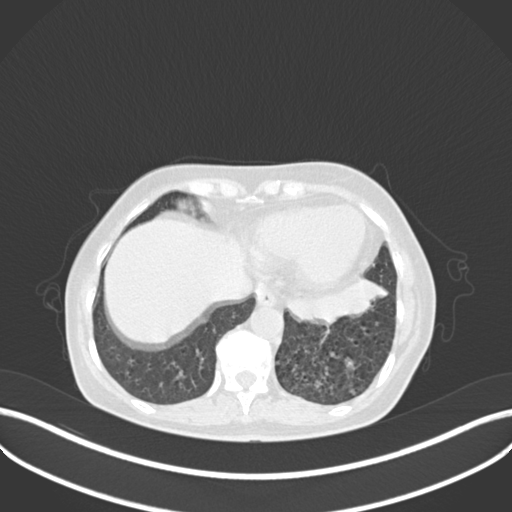
Chest CT, one axial slice; position 59 of 270 along the scan axis; reconstruction kernel B30f; 120 kVp; lung window (W 1500 / L -600 HU); 1 mm slice thickness; 512 × 512 image matrix, field of view 400 × 400 mm. Female patient, age 63 years. From the clinical record (not read from this slice): clinical TNM (as recorded): T1b N0 M0; histopathological grade: G2-3.
Outlined on this slice (rectangle marked by the reading radiologist):
- lung tumour (recorded histology: adenocarcinoma): box from (x=288, y=274) to (x=391, y=325) px